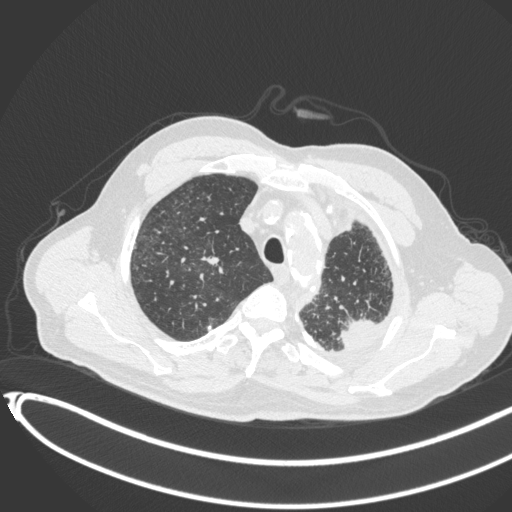
Chest CT, one axial slice; slice 350 of 451 in the series (ordered by position); reconstruction kernel B31f; lung window (W 1500 / L -600 HU); 1 mm slice thickness; 512 × 512 image matrix. Patient: male, 78 years. Case-level facts recorded for this patient, not image findings: clinical TNM (as recorded): T1c N0 M1.
Outlined on this slice (bounding box drawn by a radiologist):
- lung tumour (recorded histology: adenocarcinoma): bounding box [x1, y1, x2, y2] px = [333, 316, 381, 351]